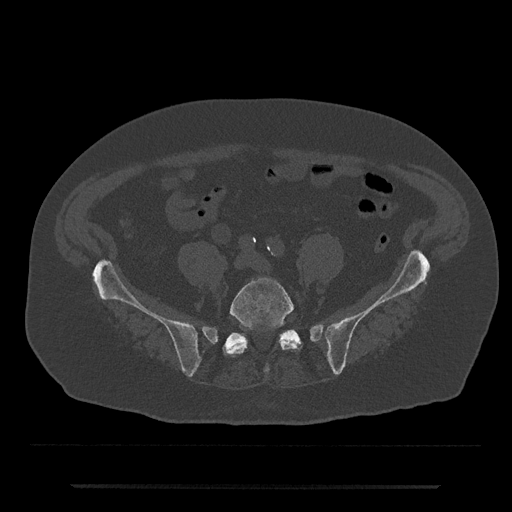
CT including the spine, one axial slice. Slice 272 of 797 in the series (ordered by position). 120 kVp. Bone window (W 1800 / L 400 HU). 0.5 mm slice thickness. 512 × 512 image matrix, field of view 434 × 434 mm. Patient: male, 80 years. From the clinical record (not read from this slice): primary cancer: prostate.
Annotated regions visible in this slice (semi-automatic segmentation, software-assisted and operator-edited):
- L5 vertebra: bounding box [x1, y1, x2, y2] px = [223, 277, 300, 372]